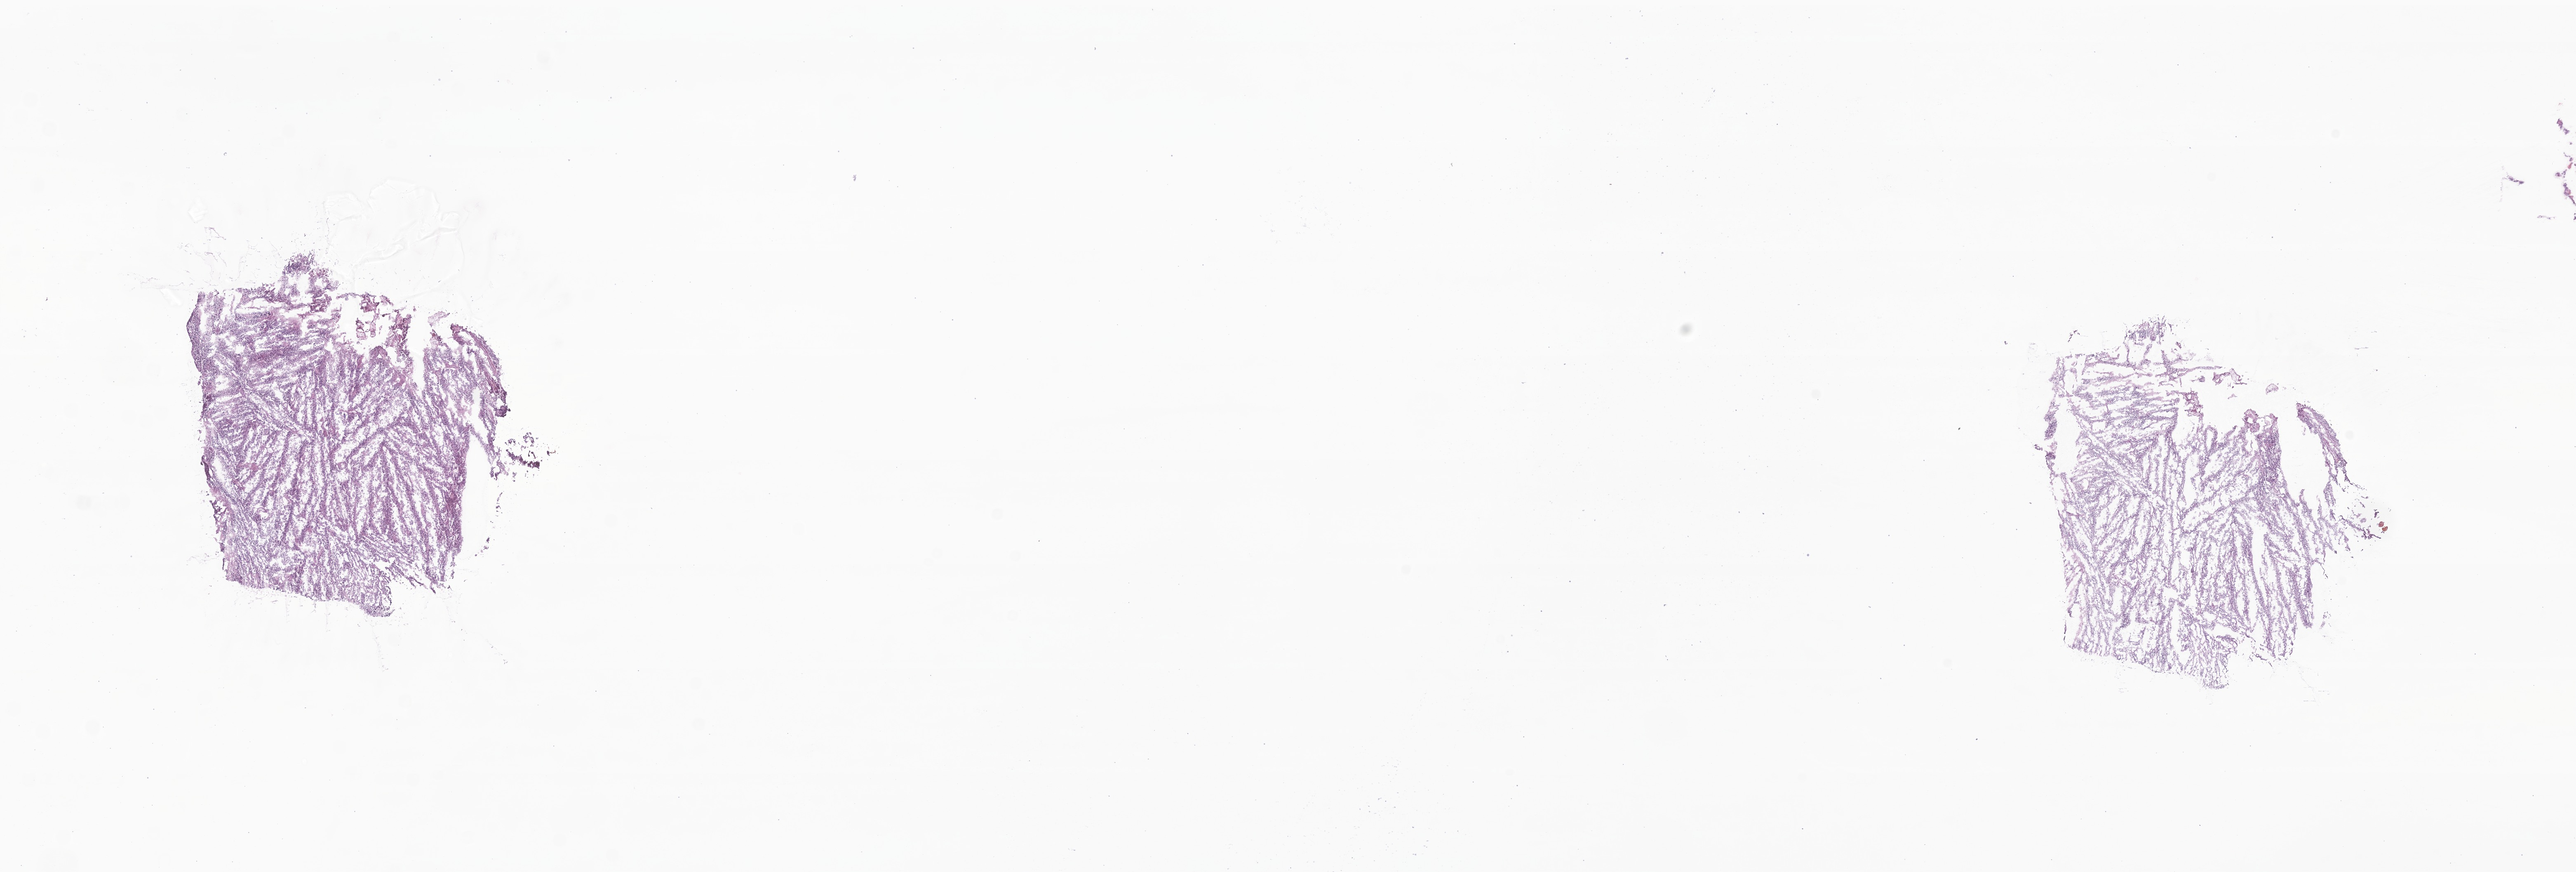
Digitized haematoxylin and eosin-stained section of tumor tissue from the brain — low-resolution overview of the scanned area, about 26.3 x 8.9 mm, frozen section. Patient male; age 161 months (13 years 5 months).
Diagnosis: Glioma, malignant.